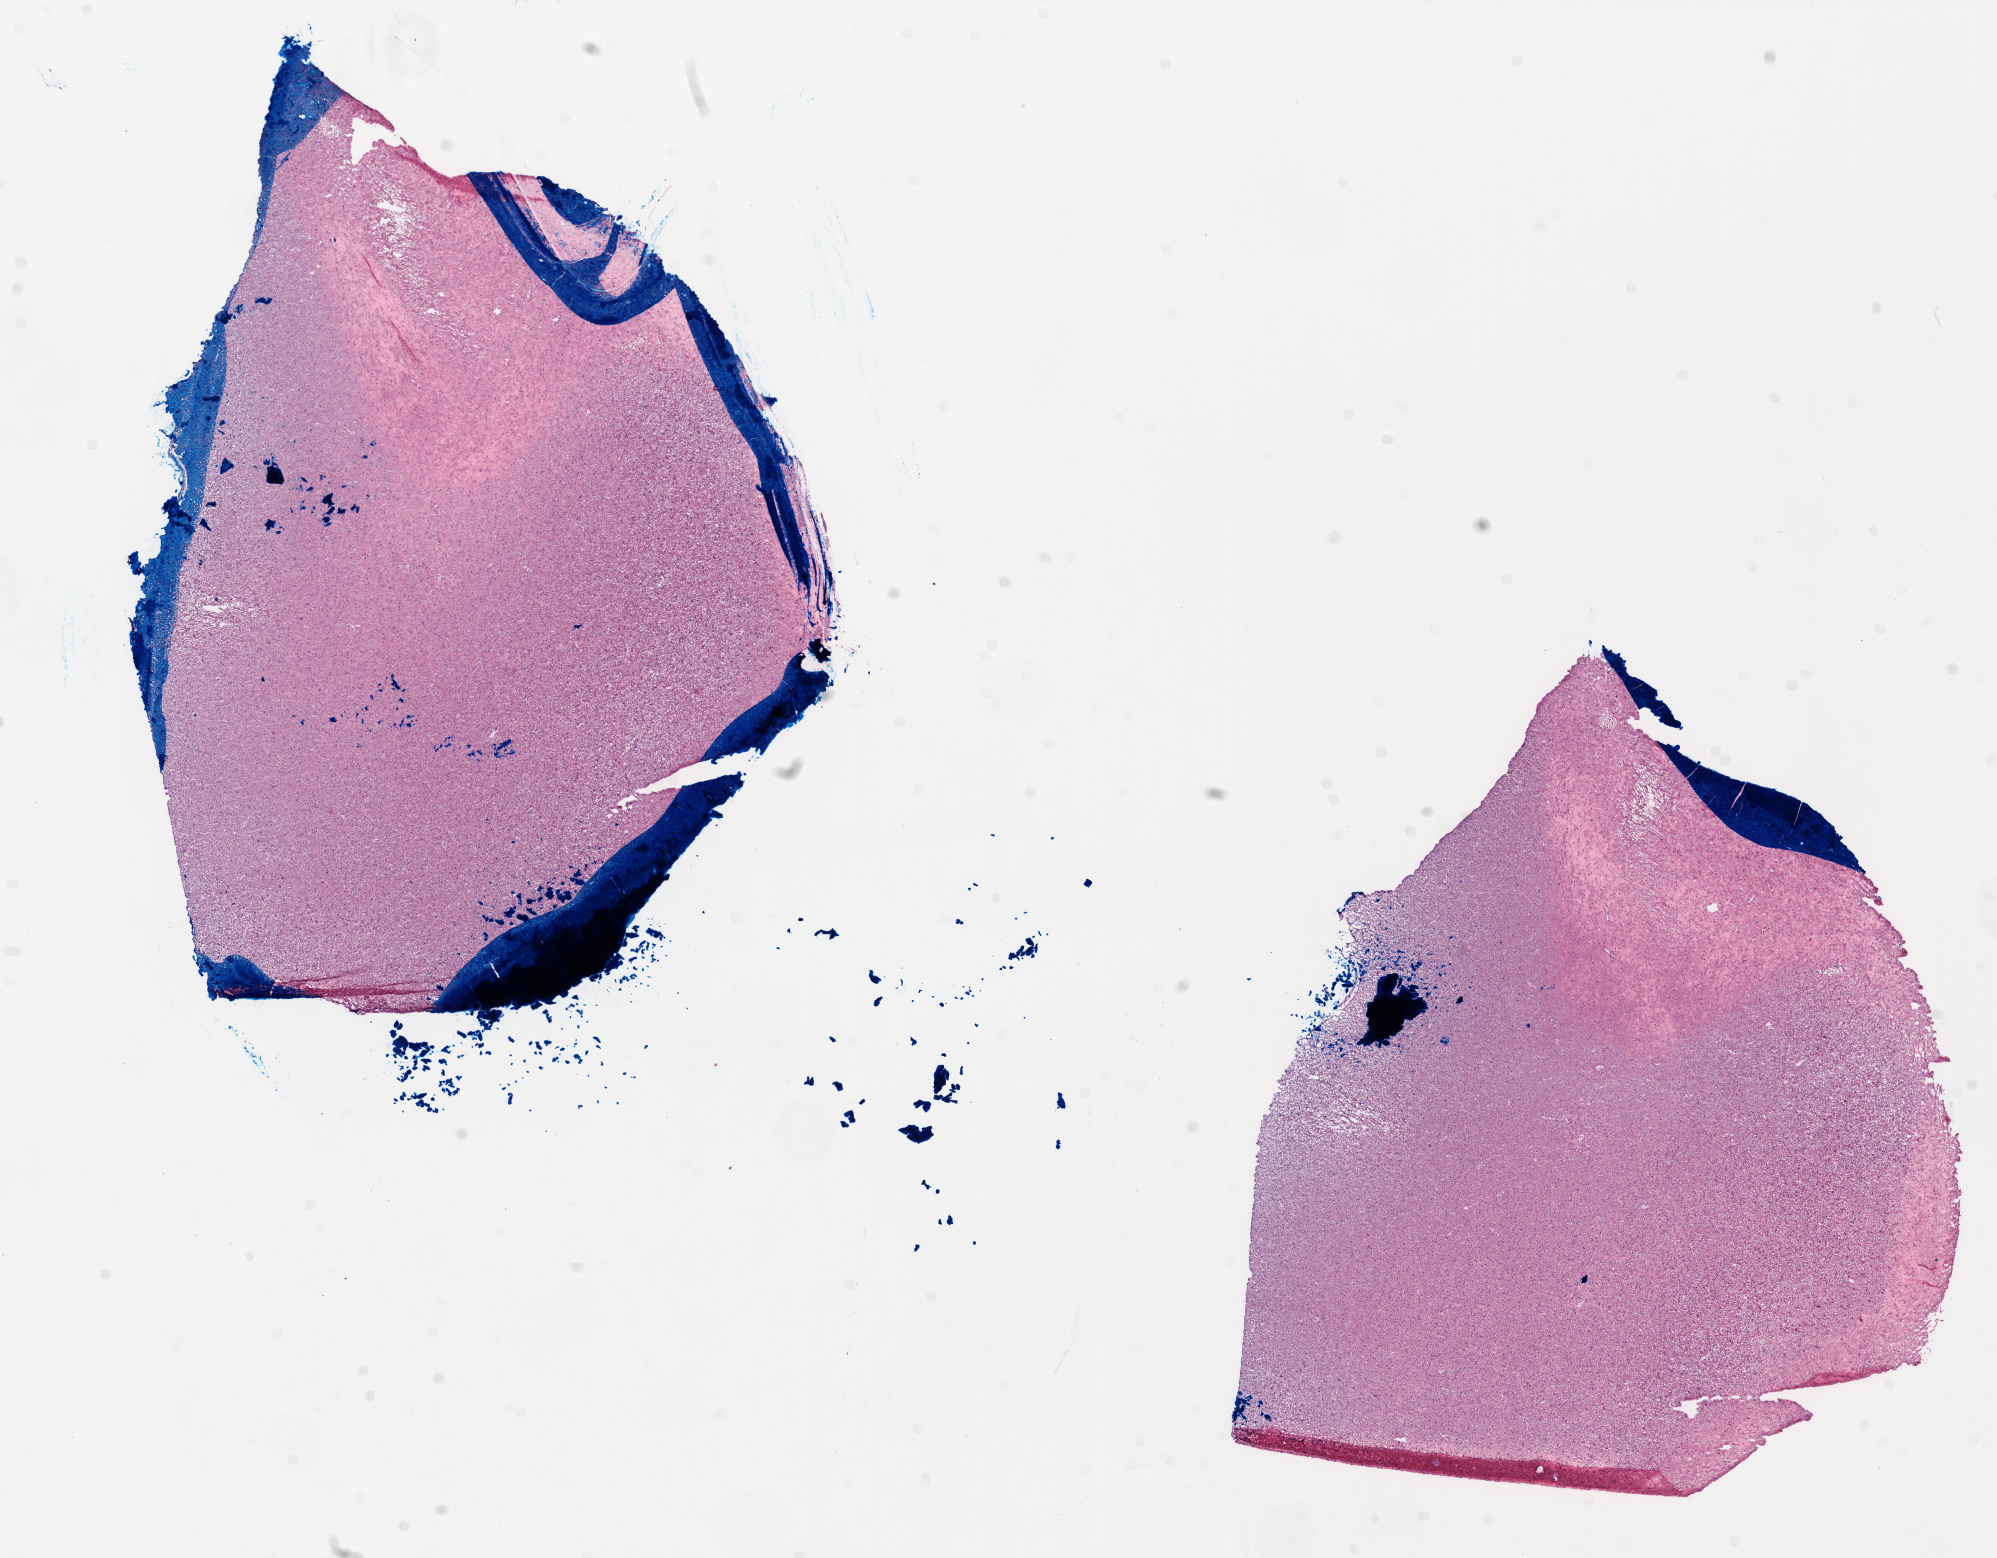
Whole-slide histology image, H&E, whole scanned area (about 16.0 x 12.5 mm, acquisition: 20x scan) shown as a low-resolution overview, frozen section from the top of the tissue portion, primary tumour sample from the brain. Female patient; age at initial diagnosis 61 years. Pathologist review of this section (percent, as recorded): tumour cells 0%, tumour nuclei 0%, normal cells 100%, stromal cells 0%, necrosis 0%.
- diagnosis: Glioblastoma